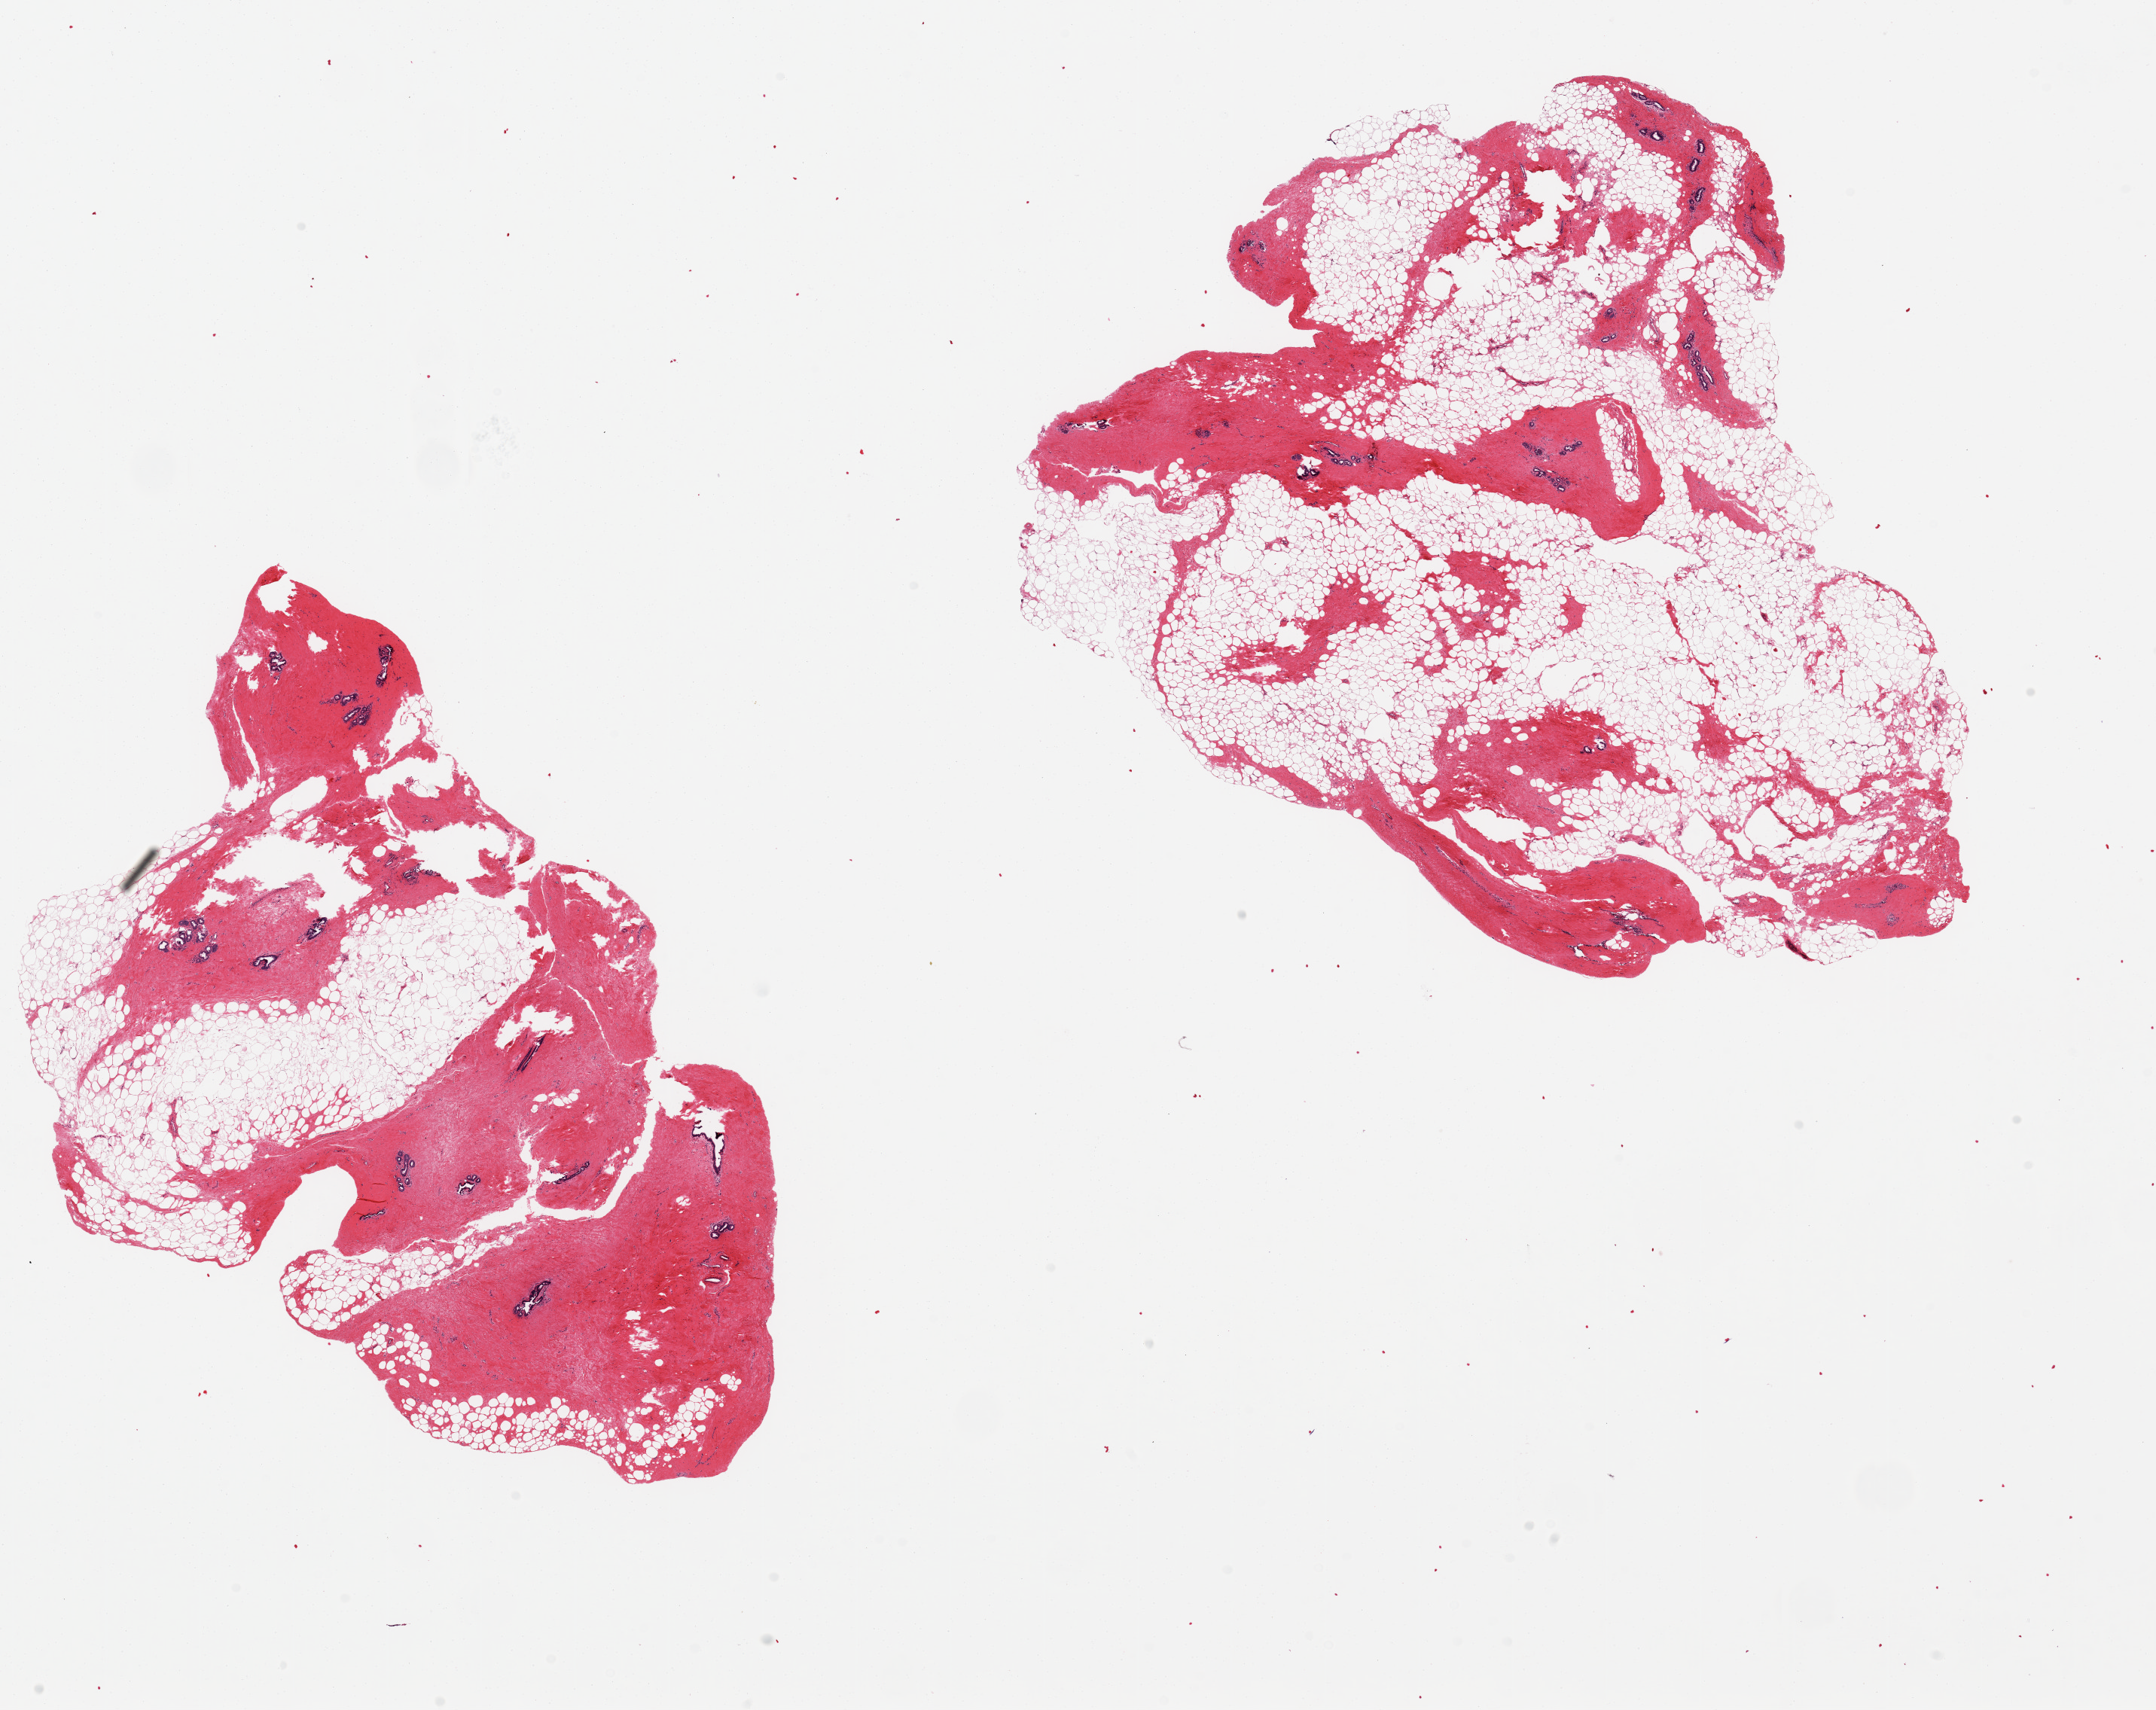
Whole-slide image, haematoxylin and eosin stain, shown as a low-resolution overview of the whole scanned area (about 22.6 x 18.0 mm, acquisition: 20x scan); PAXgene-fixed, paraffin-embedded tissue; target tissue: breast; donor tissue sample. Donor sex: male.
• reviewer comment on this tissue sample: 2 pieces ~10x6mm; Numerous ductal units visible, some, evidence of gynecomastoid hyperplasia